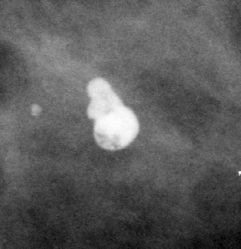
Crop from a digitized film mammogram around one marked abnormality, left breast, MLO view, BI-RADS breast density category 3 (scale 1–4).
Calcifications, morphology coarse; BI-RADS assessment category 2; benign without callback (not worked up further).